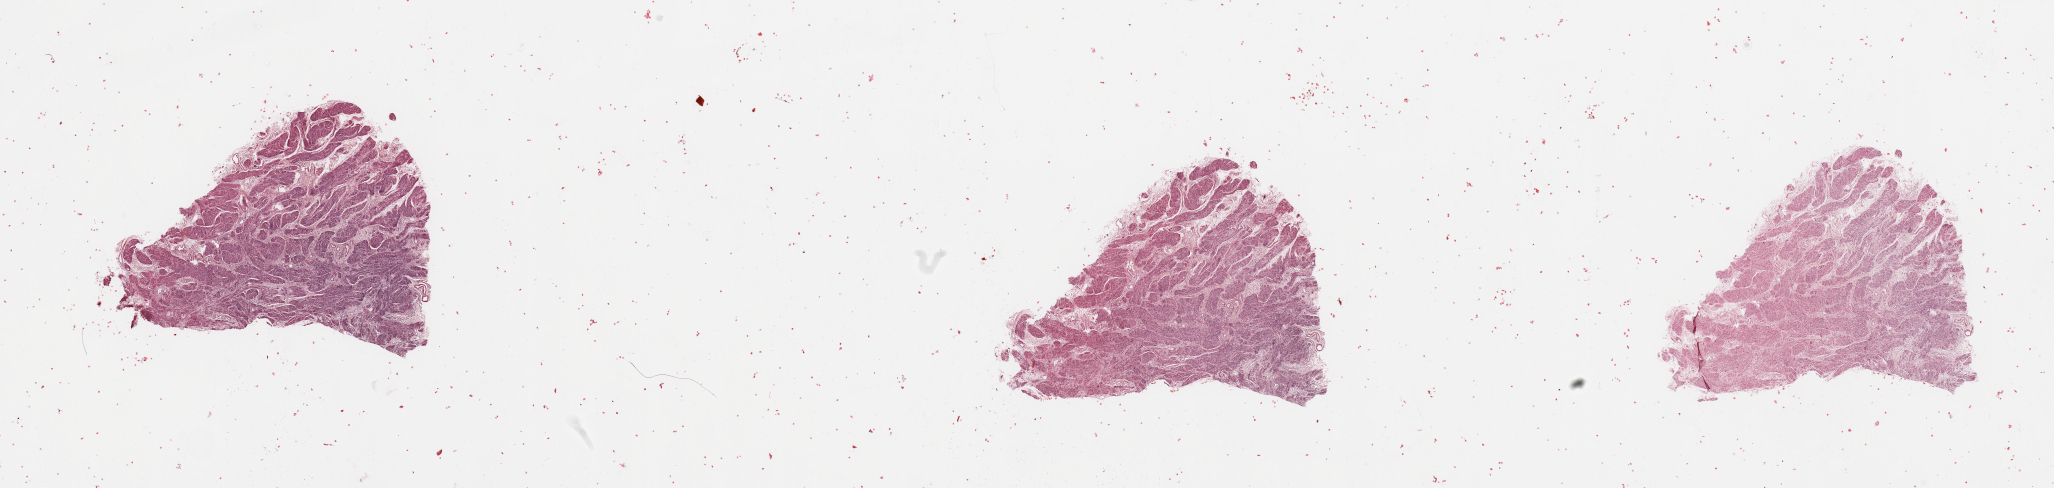
Digitized H&E tissue section (whole slide) — a low-resolution overview of the entire scanned area, about 32.5 x 7.7 mm (slide scanned at 20x). Normal (non-tumour) tissue sample, uterus. Female, 71 y/o.
This section: normal (non-tumour) tissue from the same patient. Patient diagnosis: Endometrioid adenocarcinoma, NOS.